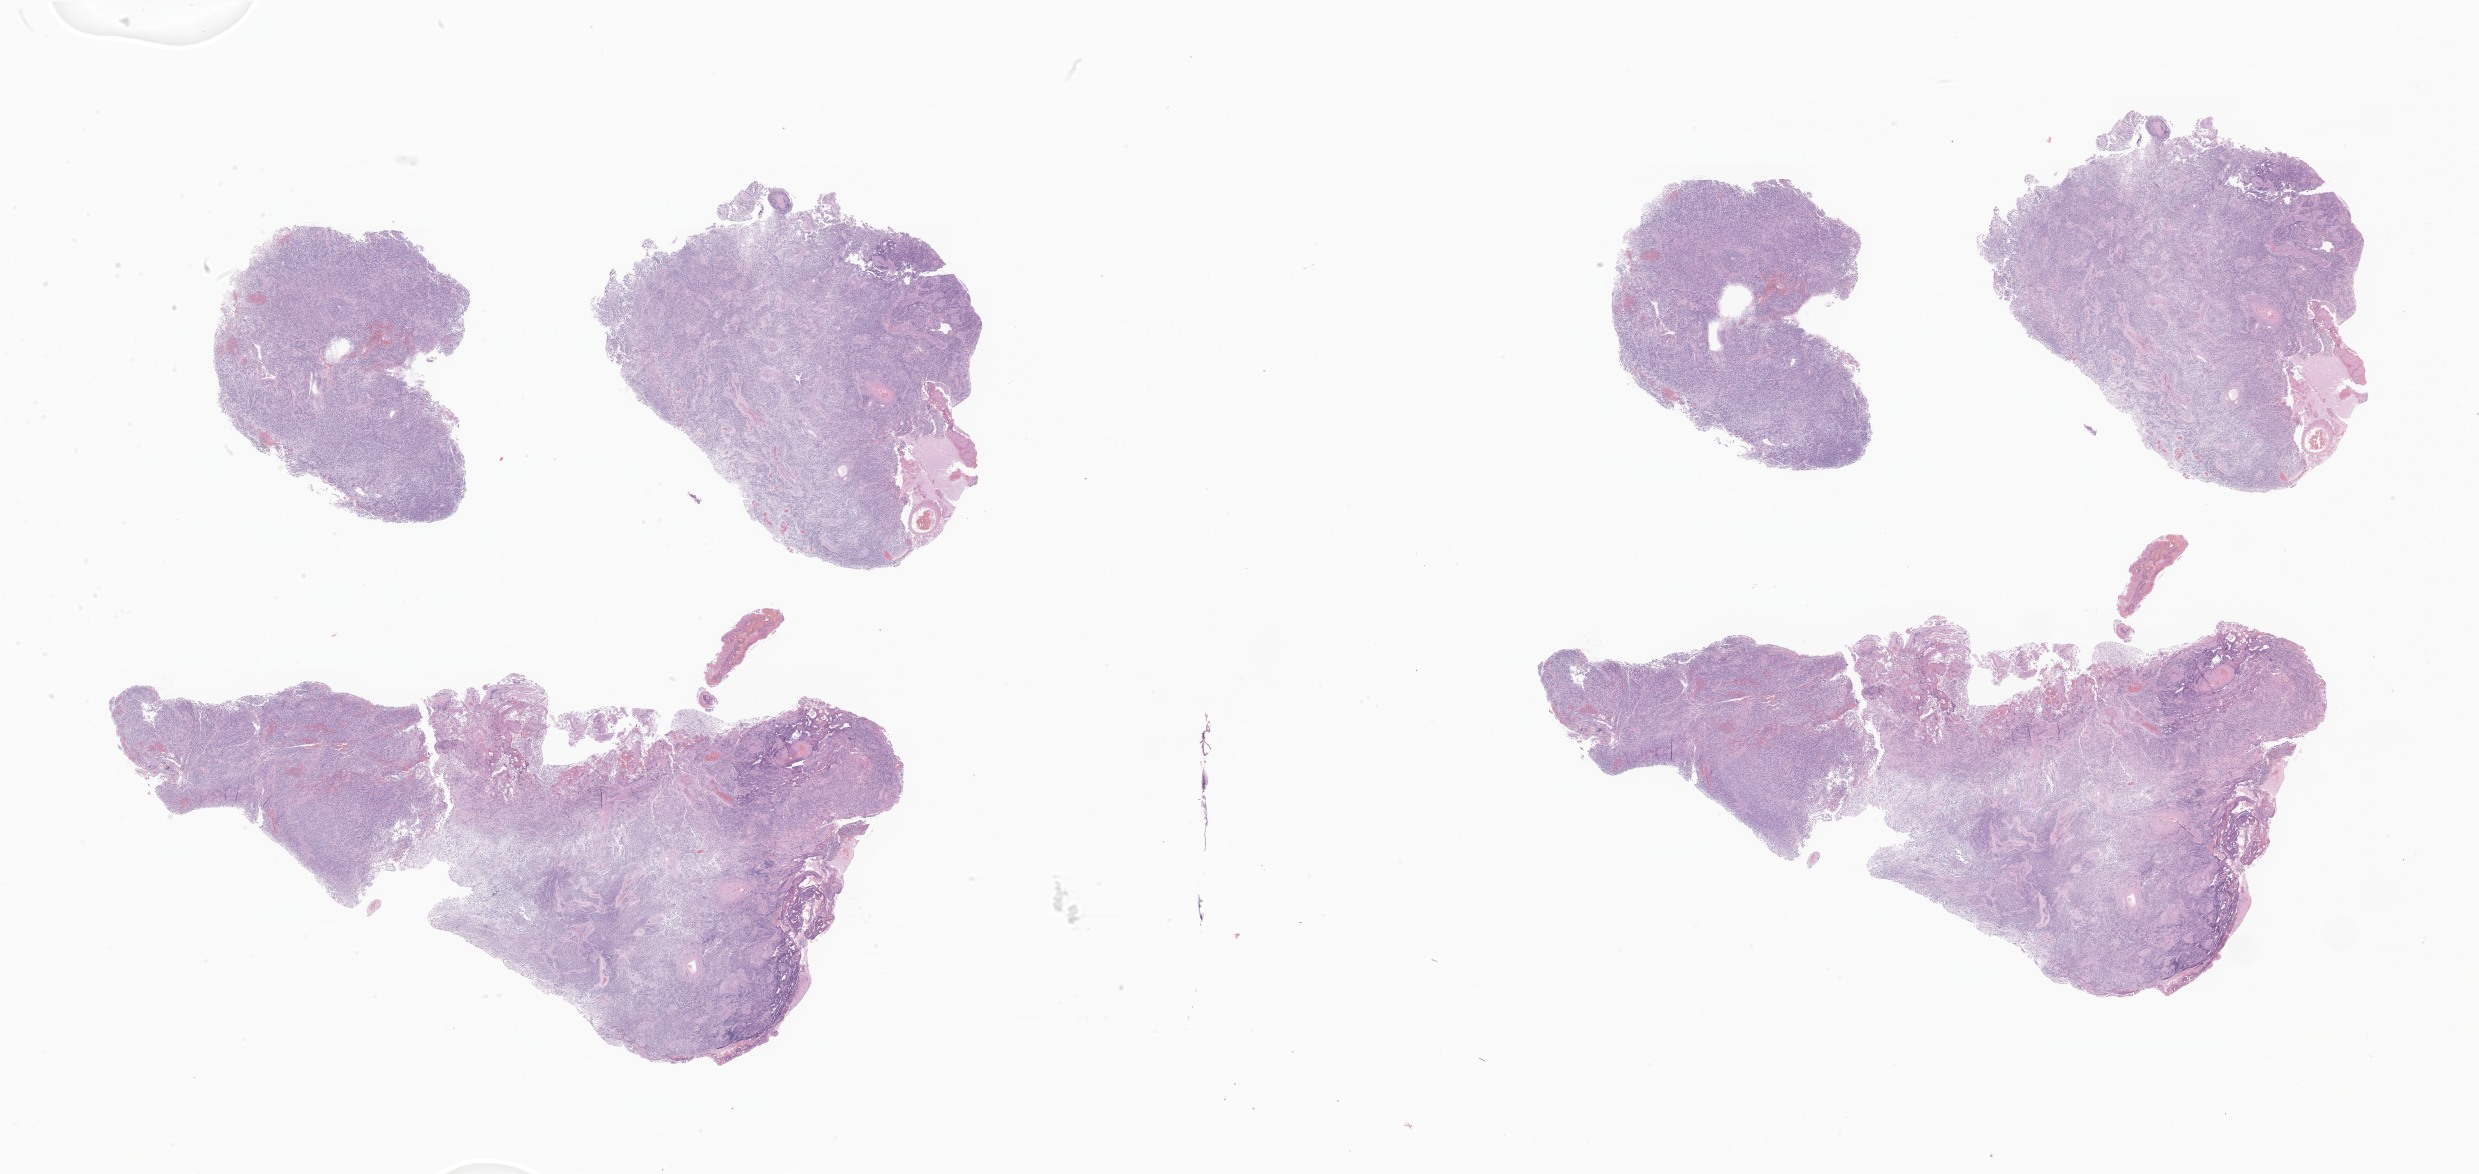
Digitized hematoxylin and eosin (H&E)-stained section of tumor tissue from the brain, whole scanned area (about 41.8 x 19.8 mm) shown as a low-resolution overview, FFPE section. Male patient, age 100 months (8 years 4 months).
- diagnosis (ICD-O-3 morphology term): Medulloblastoma, NOS